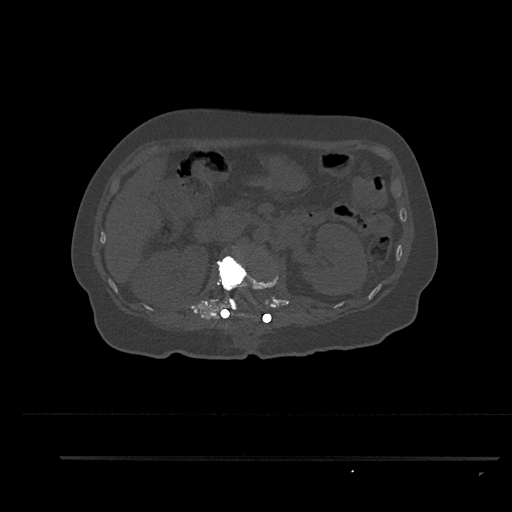
CT including the spine, one axial slice; position 200 of 797 along the scan axis; reconstruction kernel Br40s/3; 120 kVp; bone window (W 1800 / L 400 HU); 512 × 512 image matrix, field of view 408 × 408 mm. Female patient, age 44 years. From the clinical record (not read from this slice): primary cancer: renal; vertebrae with lytic lesions (as recorded): L1.
Outlined on this slice (semi-automatically segmented with operator editing):
- L1 vertebra: bounding box (x1, y1, x2, y2) in pixels: (217, 246, 278, 318)